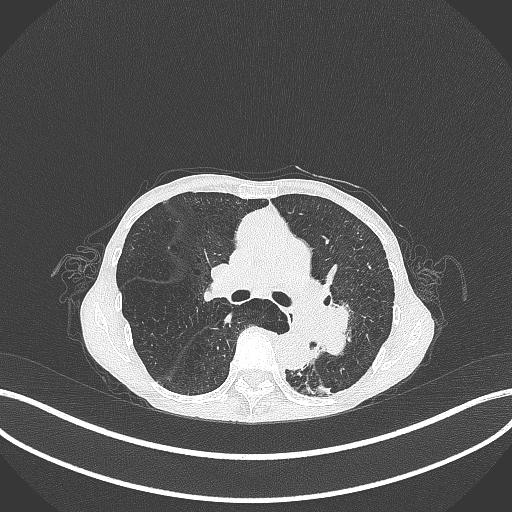
Chest CT, one axial slice. Position 168 of 347 along the scan axis. Reconstruction kernel B70f. 120 kVp. Lung window (W 1500 / L -600 HU). 512 × 512 image matrix, field of view 400 × 400 mm. Female patient, age 70 years. From the clinical record (not read from this slice): clinical TNM (as recorded): T3 N0 M0; histopathological grade: G3.
Outlined on this slice (rectangle marked by the reading radiologist):
- lung tumour (recorded histology: small cell carcinoma): bounding box [x1, y1, x2, y2] px = [307, 294, 362, 367]